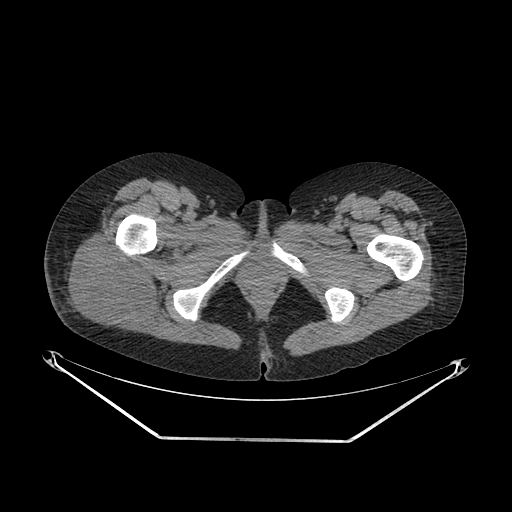
CT of an extremity soft-tissue mass (from a PET/CT study), one axial slice. Position 37 of 267 along the scan axis. Reconstruction kernel SOFT. 140 kVp. Soft-tissue window (W 400 / L 40 HU). 3.75 mm slice thickness. 512 × 512 image matrix, field of view 500 × 500 mm. Female patient. From the clinical record (not read from this slice): histological type: epithelioid sarcoma with vascular differentiation; site of the primary tumour: right buttock.
Annotated regions visible in this slice (expert contour drawn on MRI and transferred to this co-registered scan by the dataset authors):
- gross tumour volume (mass): bounding box (x1, y1, x2, y2) in pixels: (66, 234, 154, 330)